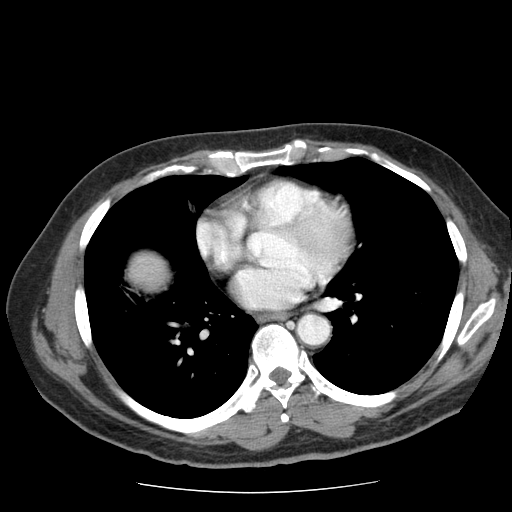
Contrast-enhanced abdominal CT (liver protocol), one axial slice; position 78 of 85 along the scan axis; reconstruction kernel STANDARD; 120 kVp; soft-tissue window (W 400 / L 40 HU); 2.5 mm slice thickness; 512 × 512 image matrix. Case-level facts recorded for this patient, not image findings: diagnosis: hepatocellular carcinoma (patient treated with transarterial chemoembolisation; whether this scan precedes or follows treatment is not stated here); TNM stage (as recorded): Stage-IIIA; Child-Pugh class: A; tumour differentiation: well differentiated.
Annotated regions visible in this slice (semi-automatic segmentation, software-assisted and operator-edited):
- liver parenchyma outside the tumour (the mass and vessels are separate outlines, so this box may not span the whole liver): bounding box <130,252,168,288> (left, top, right, bottom; pixels)